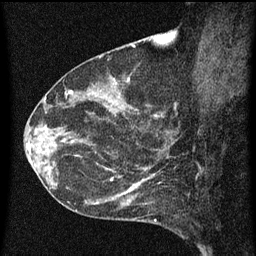
Breast MRI (dynamic contrast-enhanced), one sagittal slice; position 29 of 60 along the scan axis; dynamic contrast-enhanced series, image 2 of 3 at this slice position (ordered by acquisition); 1.5 T; TE 4.2 ms, TR 8 ms; 256 × 256 image matrix. Patient: female, 54 years.
Structures marked on this image (semi-automatic segmentation, software-assisted and operator-edited):
- analysis volume of interest (the breast-tissue region the enhancement analysis was run in; not a lesion): bounding box (x1, y1, x2, y2) in pixels: (49, 138, 164, 209)
- tumour enhancement mask (voxels above the 70 % enhancement threshold inside the analysis volume of interest): (50, 138, 161, 205)